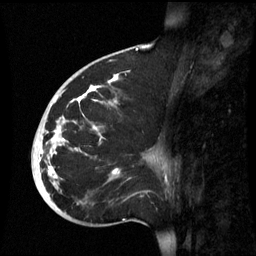
Breast MRI (dynamic contrast-enhanced), one sagittal slice. Slice 31 of 60 in the series (ordered by position). Dynamic contrast-enhanced series, image 2 of 3 at this slice position (ordered by acquisition). 1.5 T. TE 4.2 ms, TR 8.9 ms. 256 × 256 image matrix, field of view 220 × 220 mm. Female patient, age 35 years. From the clinical record (not read from this slice): setting: breast cancer imaged before/during neoadjuvant chemotherapy; receptor status: HR-positive, HER2-negative.
Structures marked on this image (semi-automatic segmentation, software-assisted and operator-edited):
- analysis volume of interest (the breast-tissue region the enhancement analysis was run in; not a lesion): box from (x=32, y=74) to (x=164, y=221) px
- tumour enhancement mask (voxels above the 70 % enhancement threshold inside the analysis volume of interest): (x=39, y=74)–(x=118, y=179)